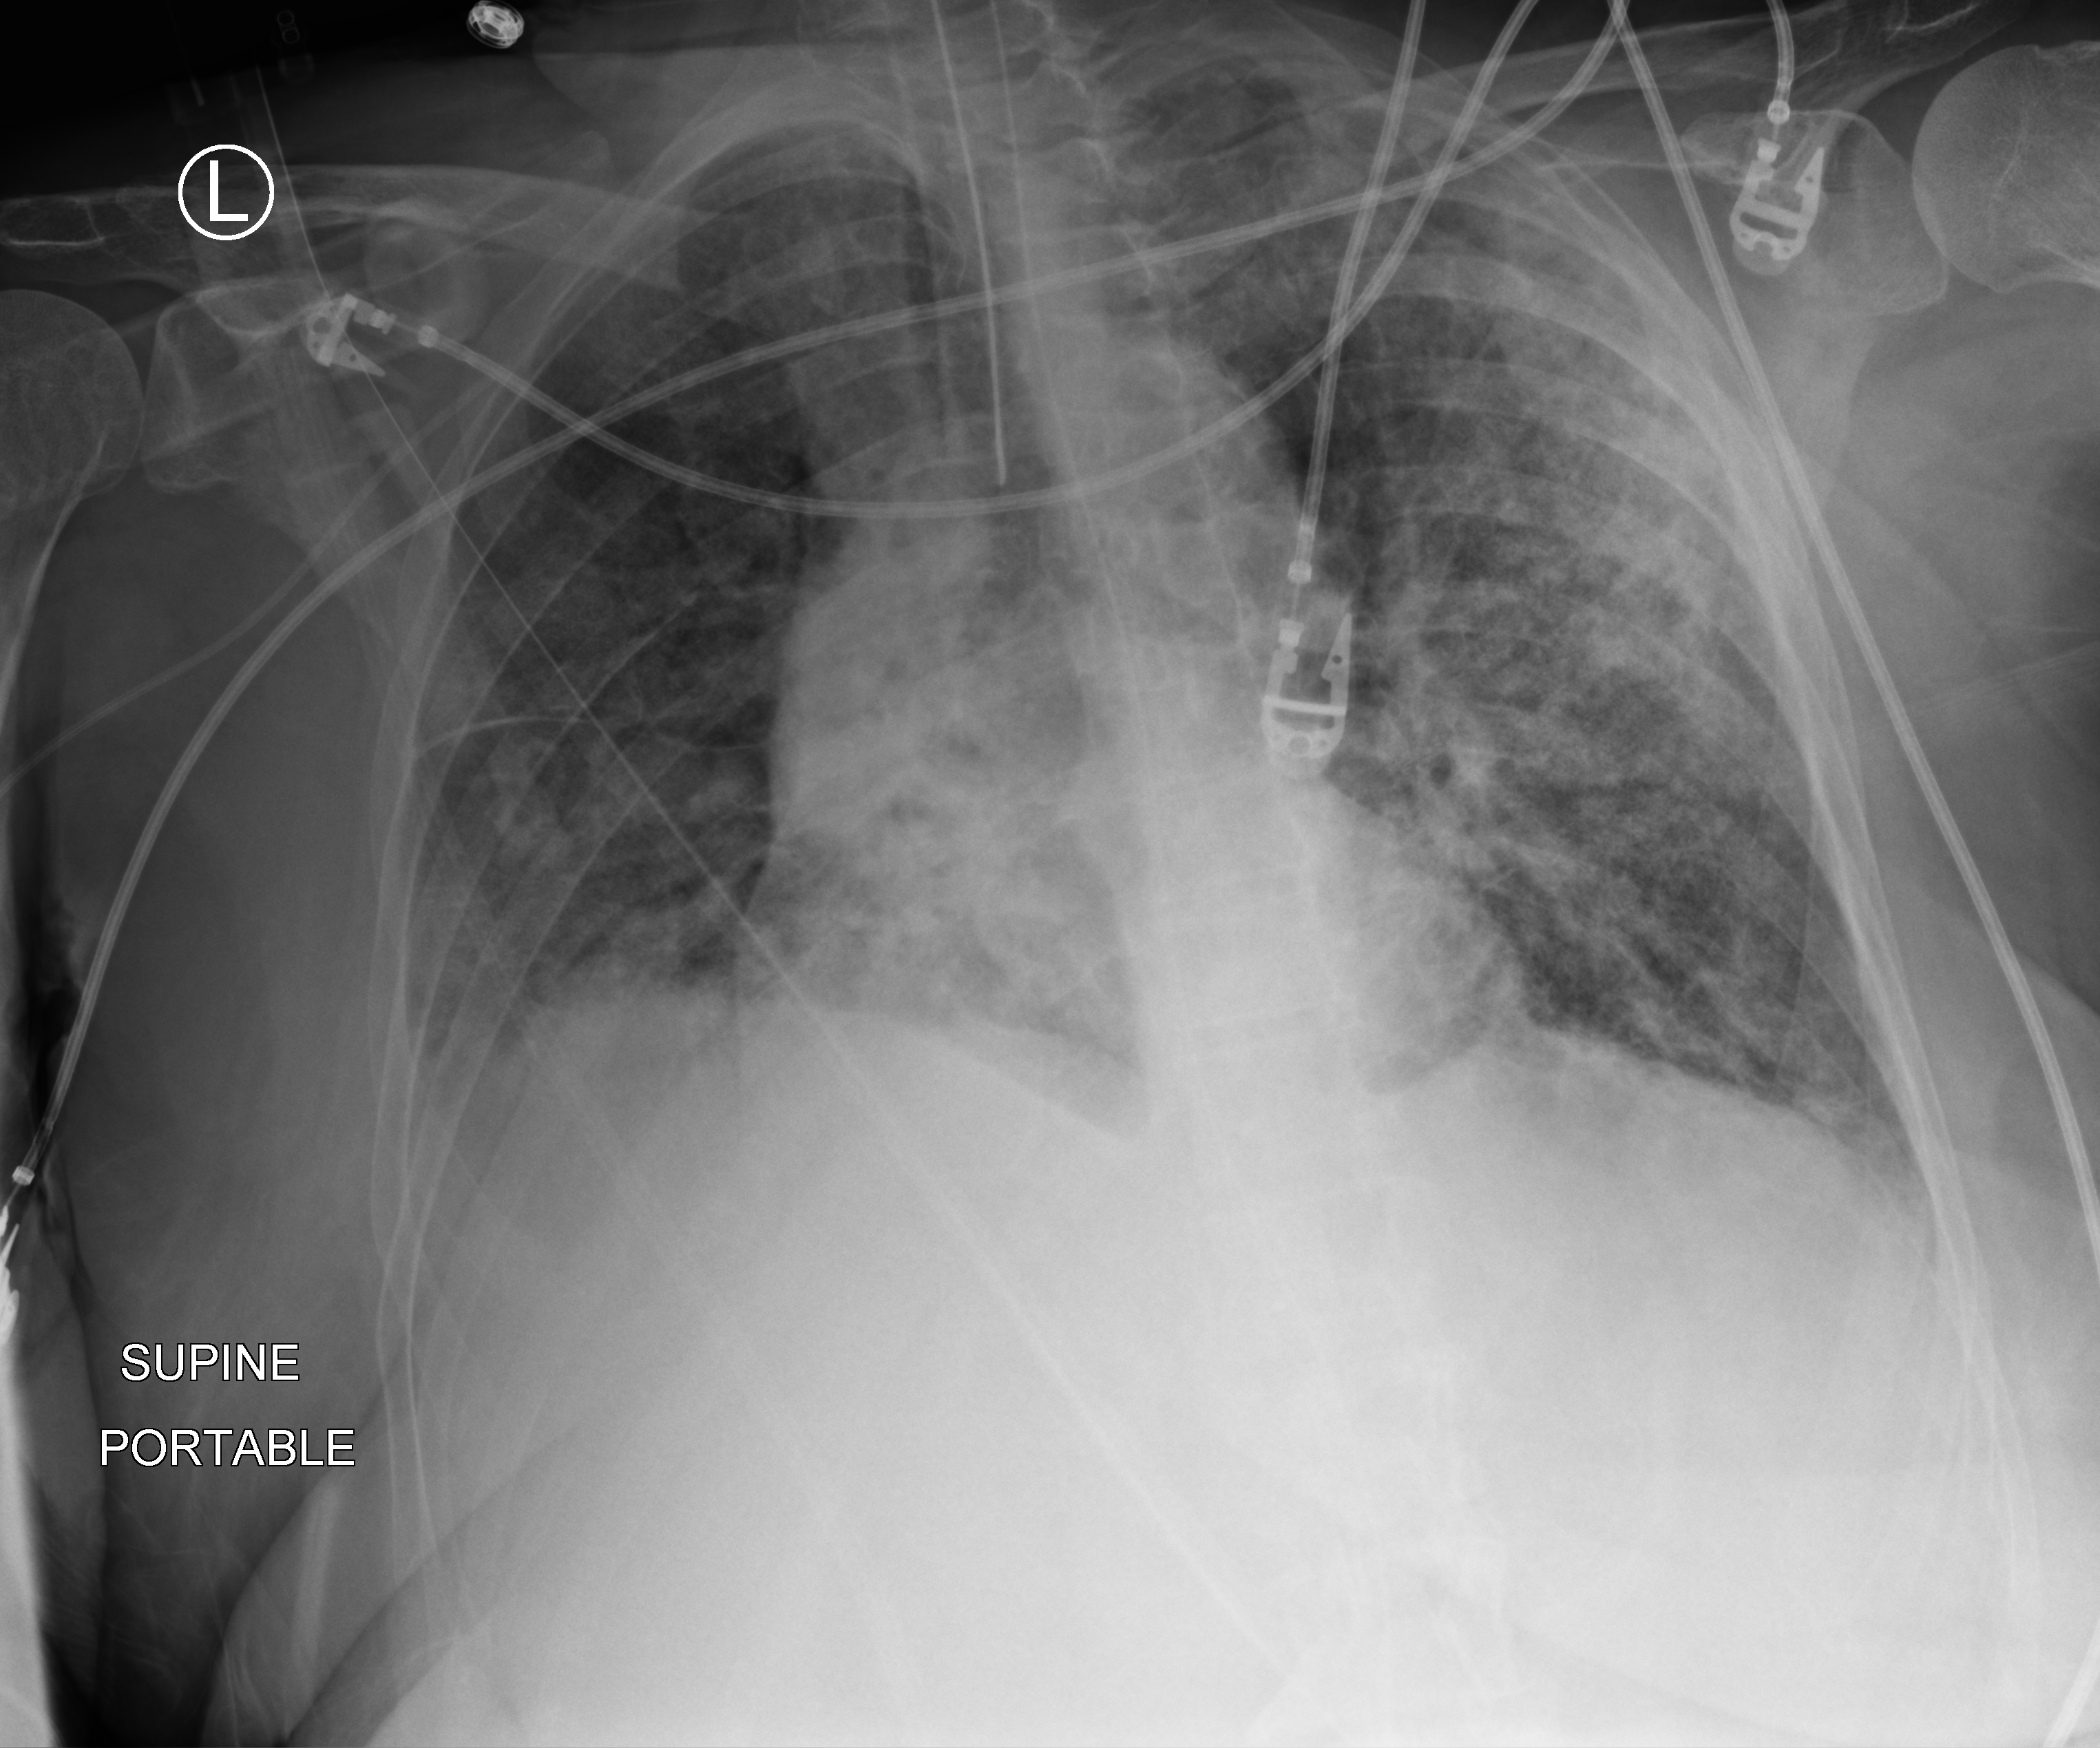
Bedside chest radiograph (computed radiography). Female patient hospitalised with COVID-19, age 75–90 years.
From the hospital-stay record, not from the radiograph (when in the stay this image was taken is not recorded): chronic kidney disease (admission record): no; mechanically ventilated during this hospital stay: yes.